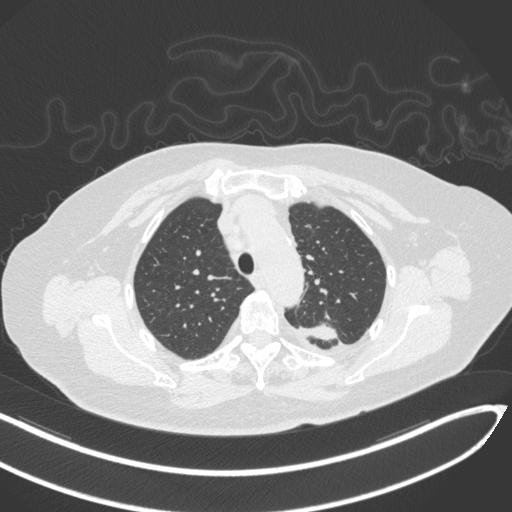
Chest CT, one axial slice; reconstruction kernel B31f; lung window (W 1500 / L -600 HU); 1 mm slice thickness; 512 × 512 image matrix, field of view 400 × 400 mm. Patient: female, 76 years. From the clinical record (not read from this slice): clinical TNM (as recorded): T1c N0 M0.
Structures marked on this image (rectangle marked by the reading radiologist):
- lung tumour (recorded histology: adenocarcinoma): bounding box [x1, y1, x2, y2] px = [300, 319, 348, 347]